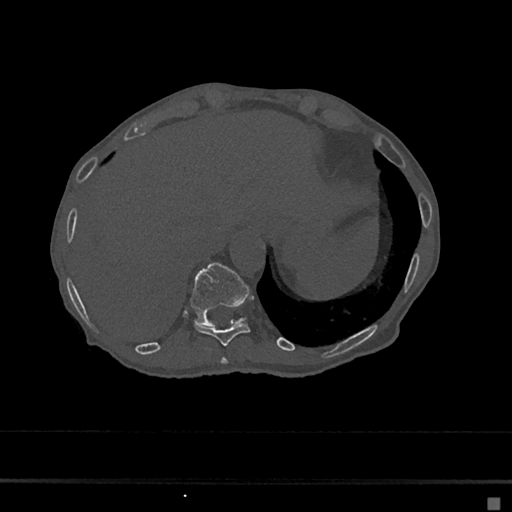
CT including the spine, one axial slice. Position 207 of 797 along the scan axis. 120 kVp. Bone window (W 1800 / L 400 HU). 512 × 512 image matrix, field of view 360 × 360 mm. Patient: female, 68 years. Case-level facts recorded for this patient, not image findings: primary cancer: renal.
Outlined on this slice (semi-automatically segmented with operator editing):
- T10 vertebra: bounding box [x1, y1, x2, y2] px = [194, 323, 250, 346]
- T11 vertebra: [191, 263, 250, 326]
- T9 vertebra: [221, 357, 228, 365]